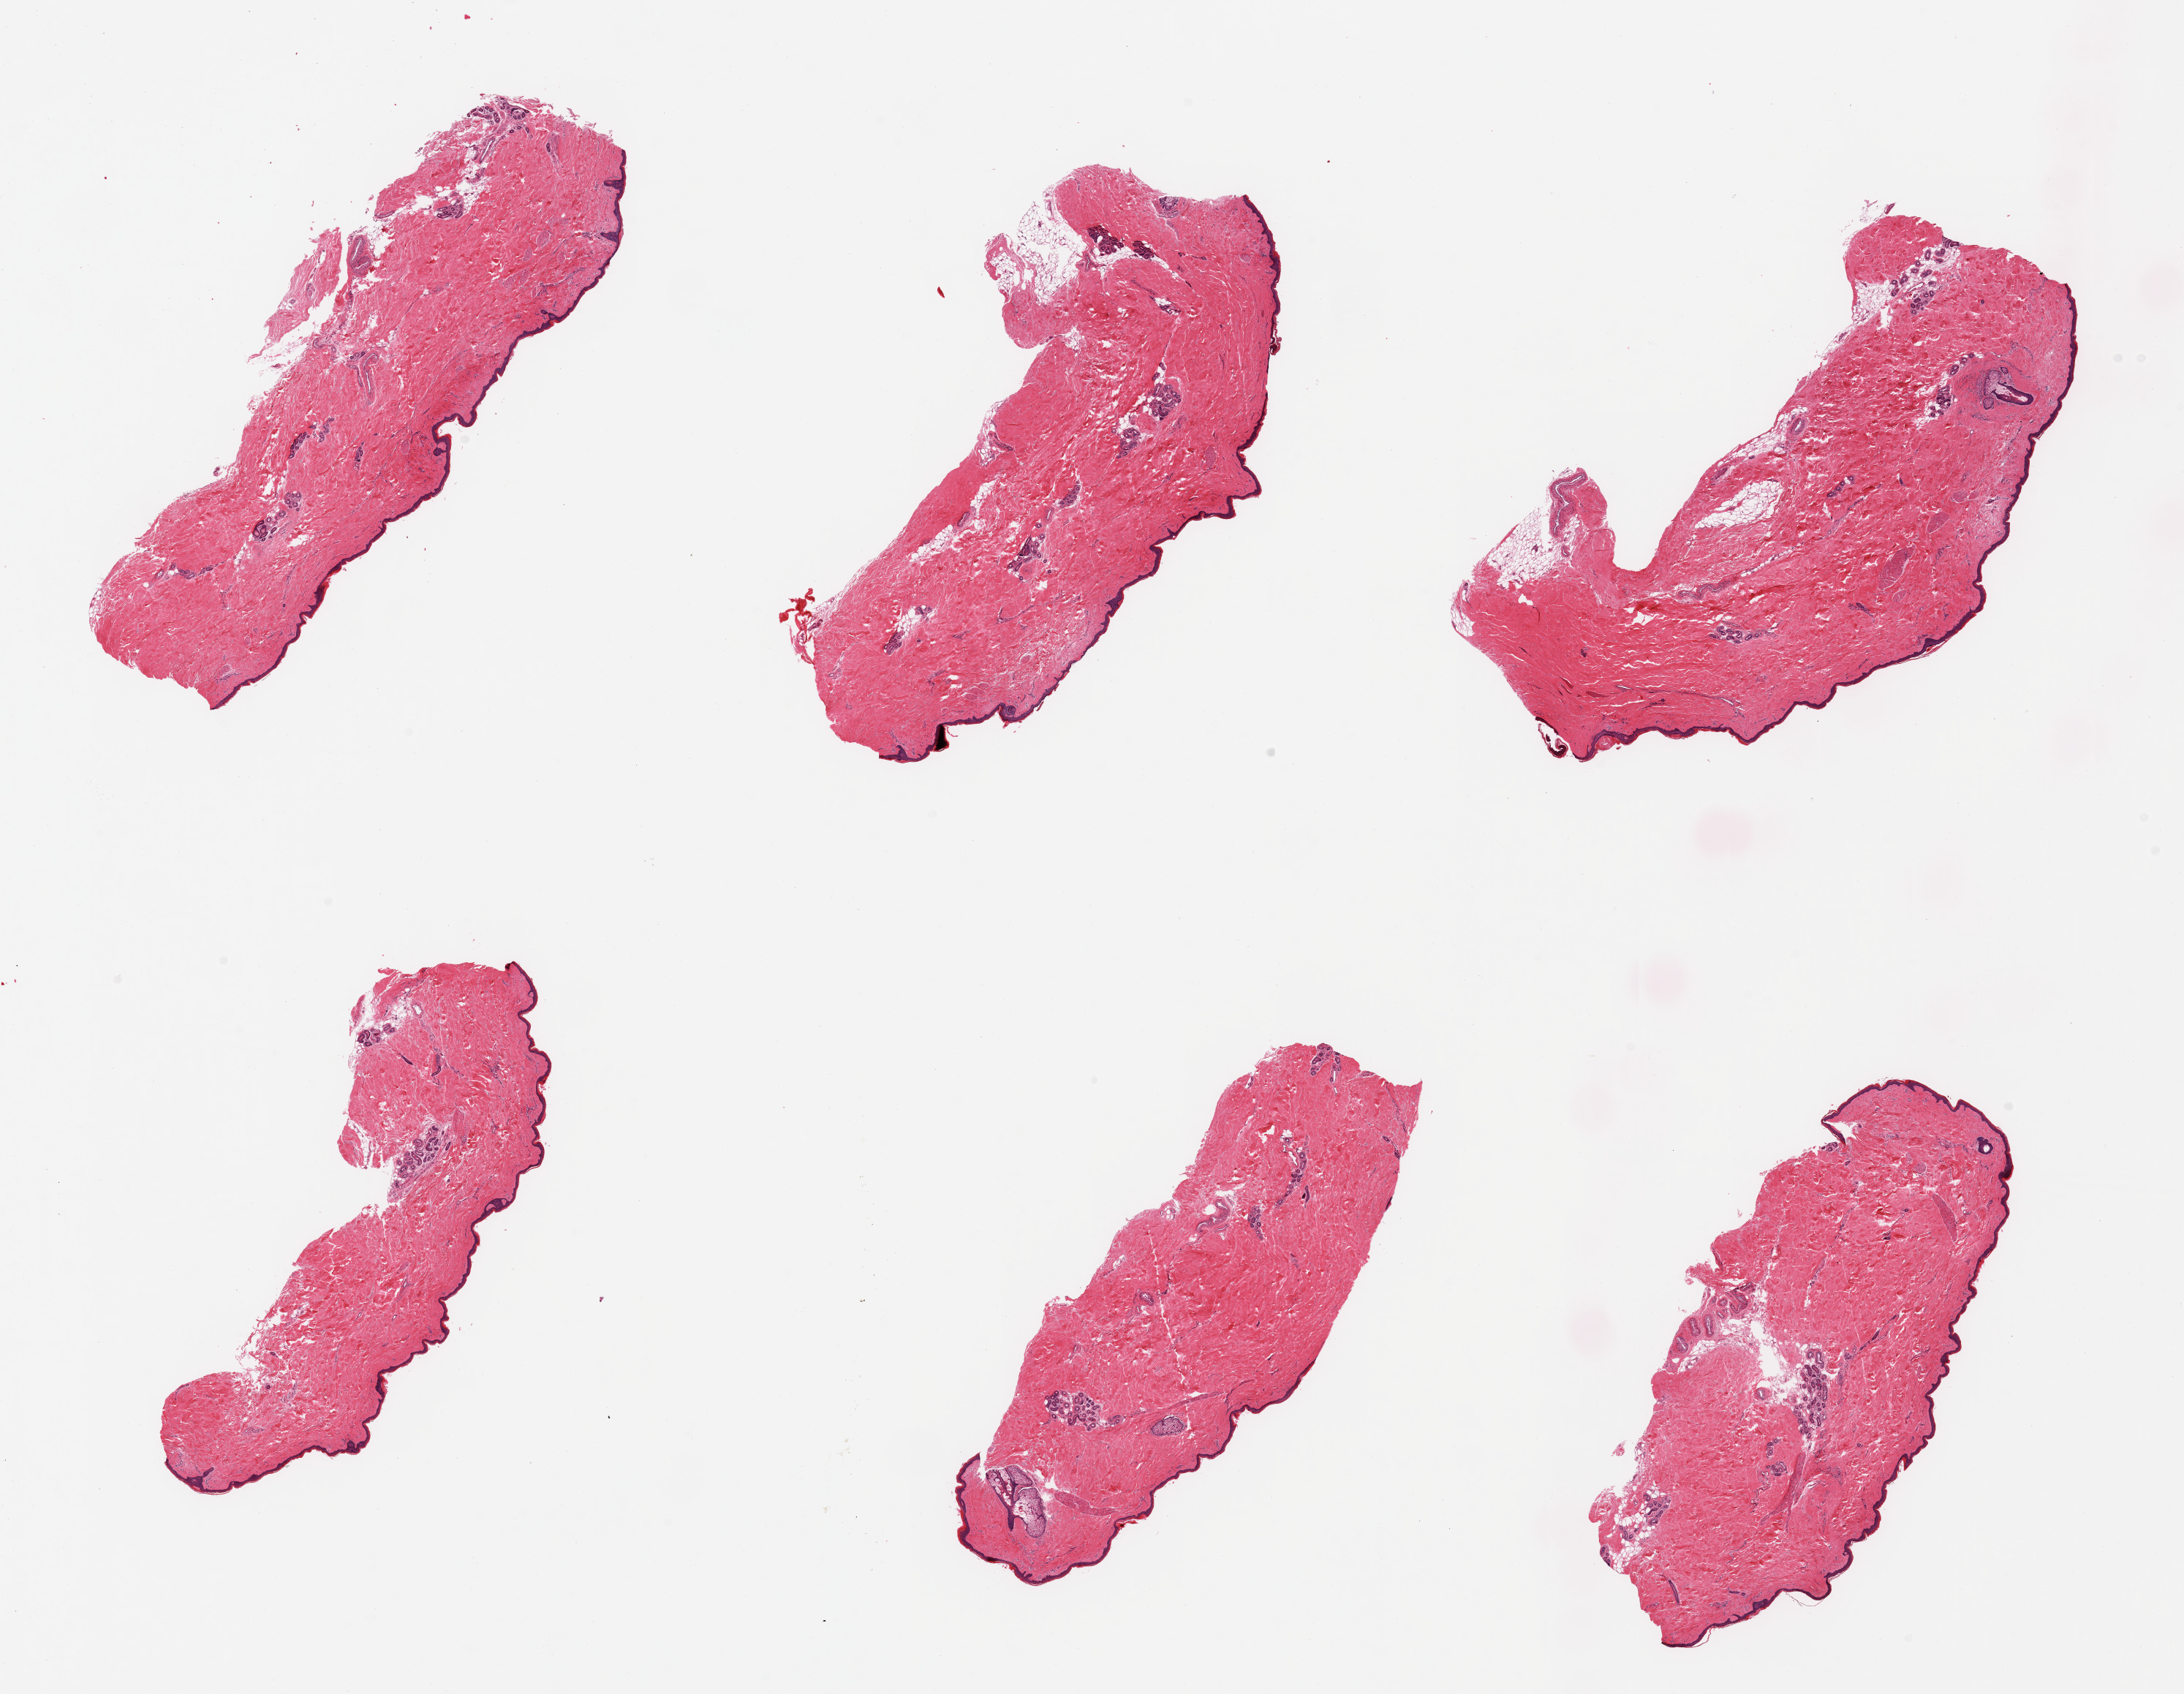
Digitized haematoxylin and eosin-stained section — shown as a low-resolution overview of the whole scanned area (about 23.6 x 18.3 mm, from a 20x scan); PAXgene-fixed paraffin-embedded (PFPE) section; sampled site (target tissue): skin of lower leg; donor tissue sample. Donor: male.
• review note (as recorded): 6 pieces; essentially well trimmed; insignificant subcutaneous and periadnexal fat; epidermis measures 33 microns